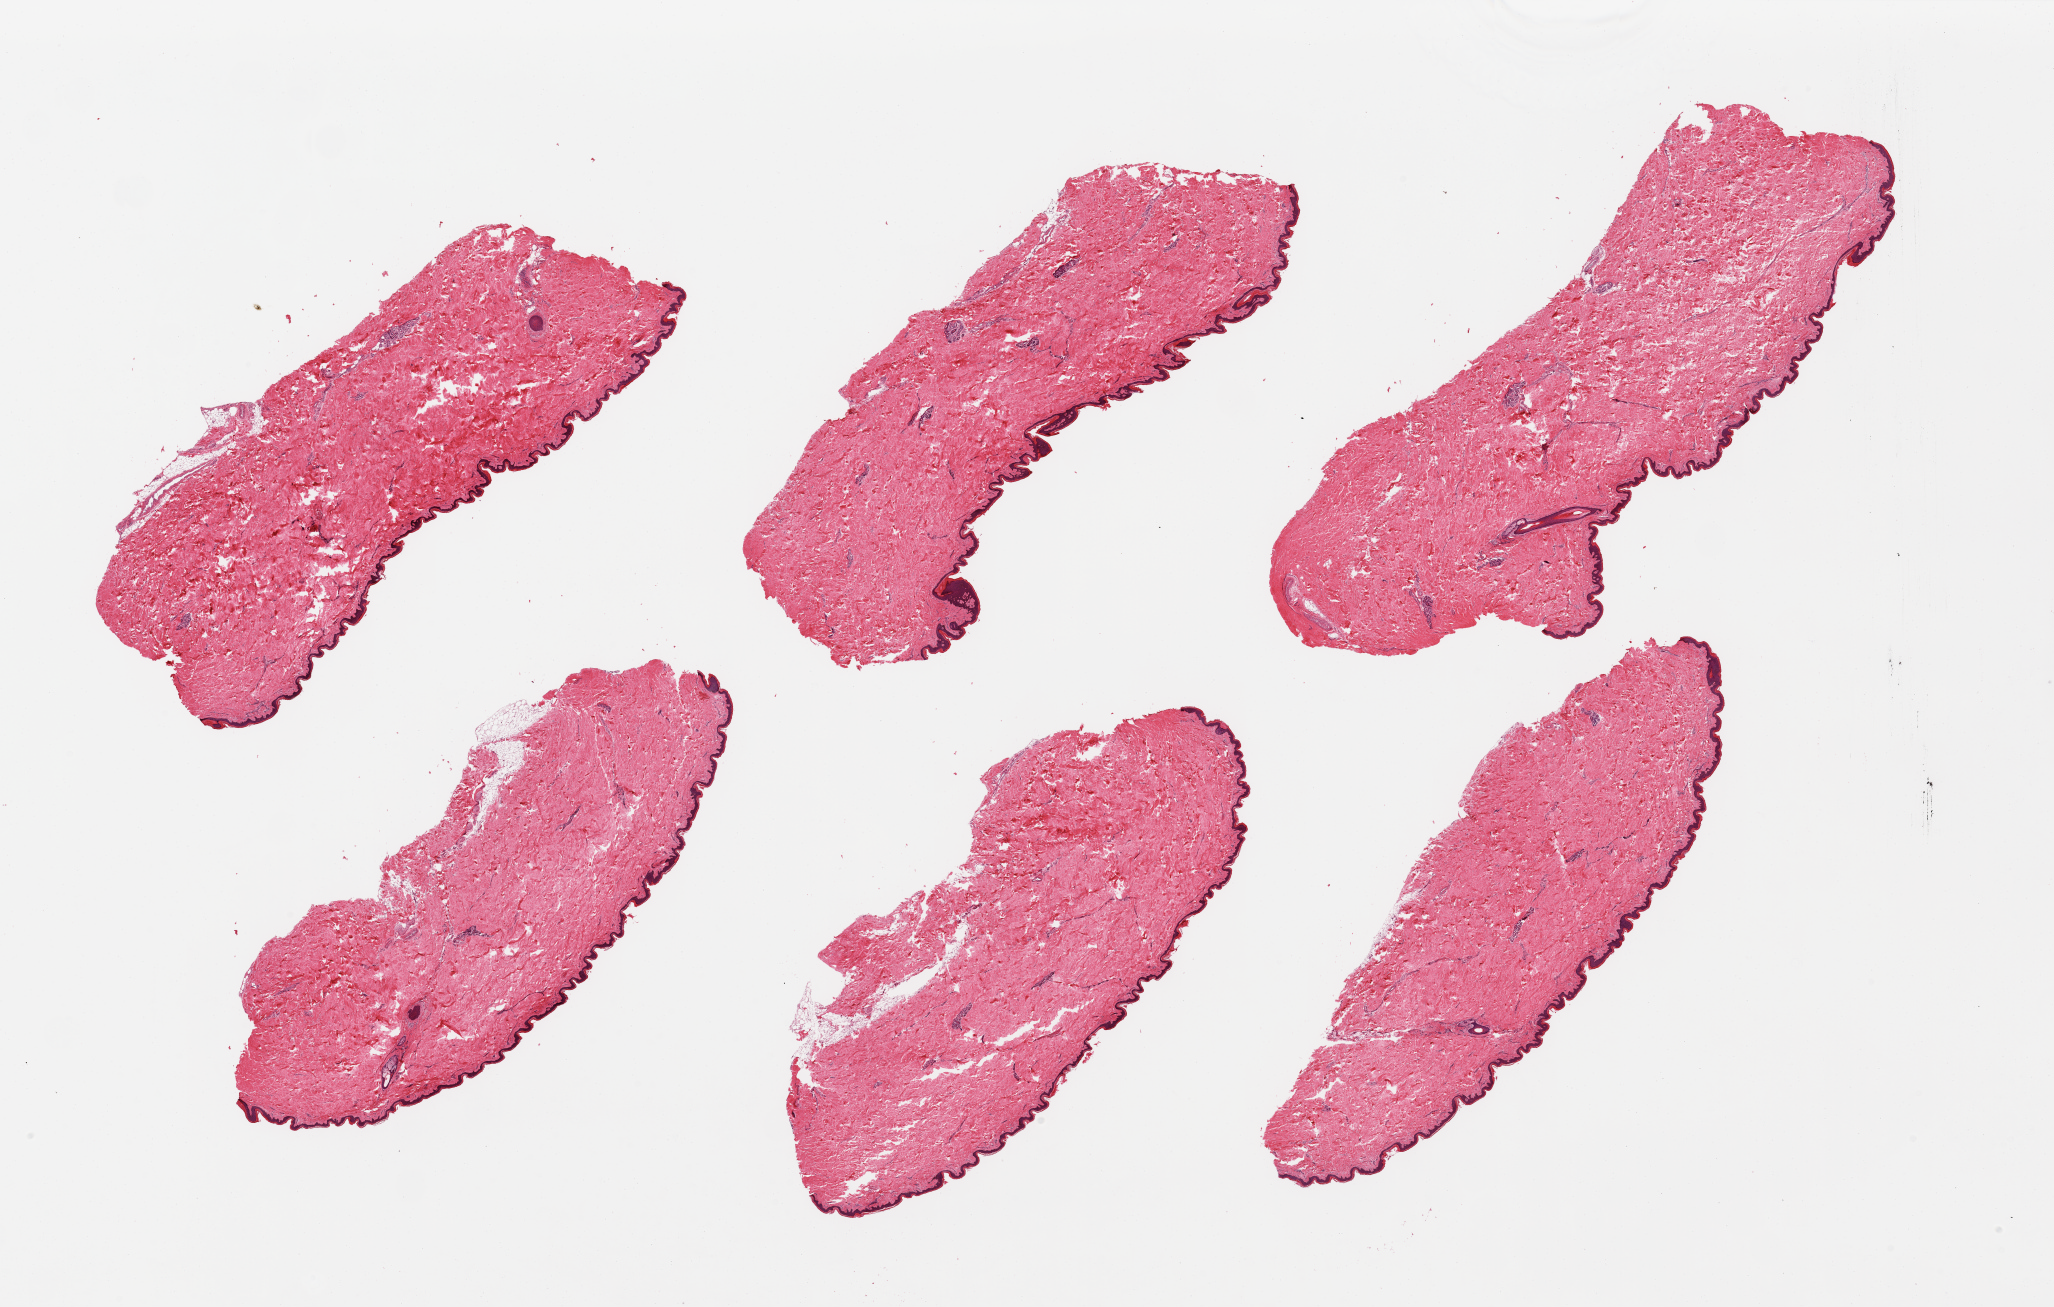
Digitized hematoxylin and eosin (H&E)-stained section, low-resolution overview of the scanned area, about 32.5 x 20.7 mm, PAXgene-fixed, paraffin-embedded tissue, target tissue: skin of suprapubic region, donor tissue sample. Donor sex: male.
Review note (as recorded): 6 pieces; well trimmed with minimal attached fat.